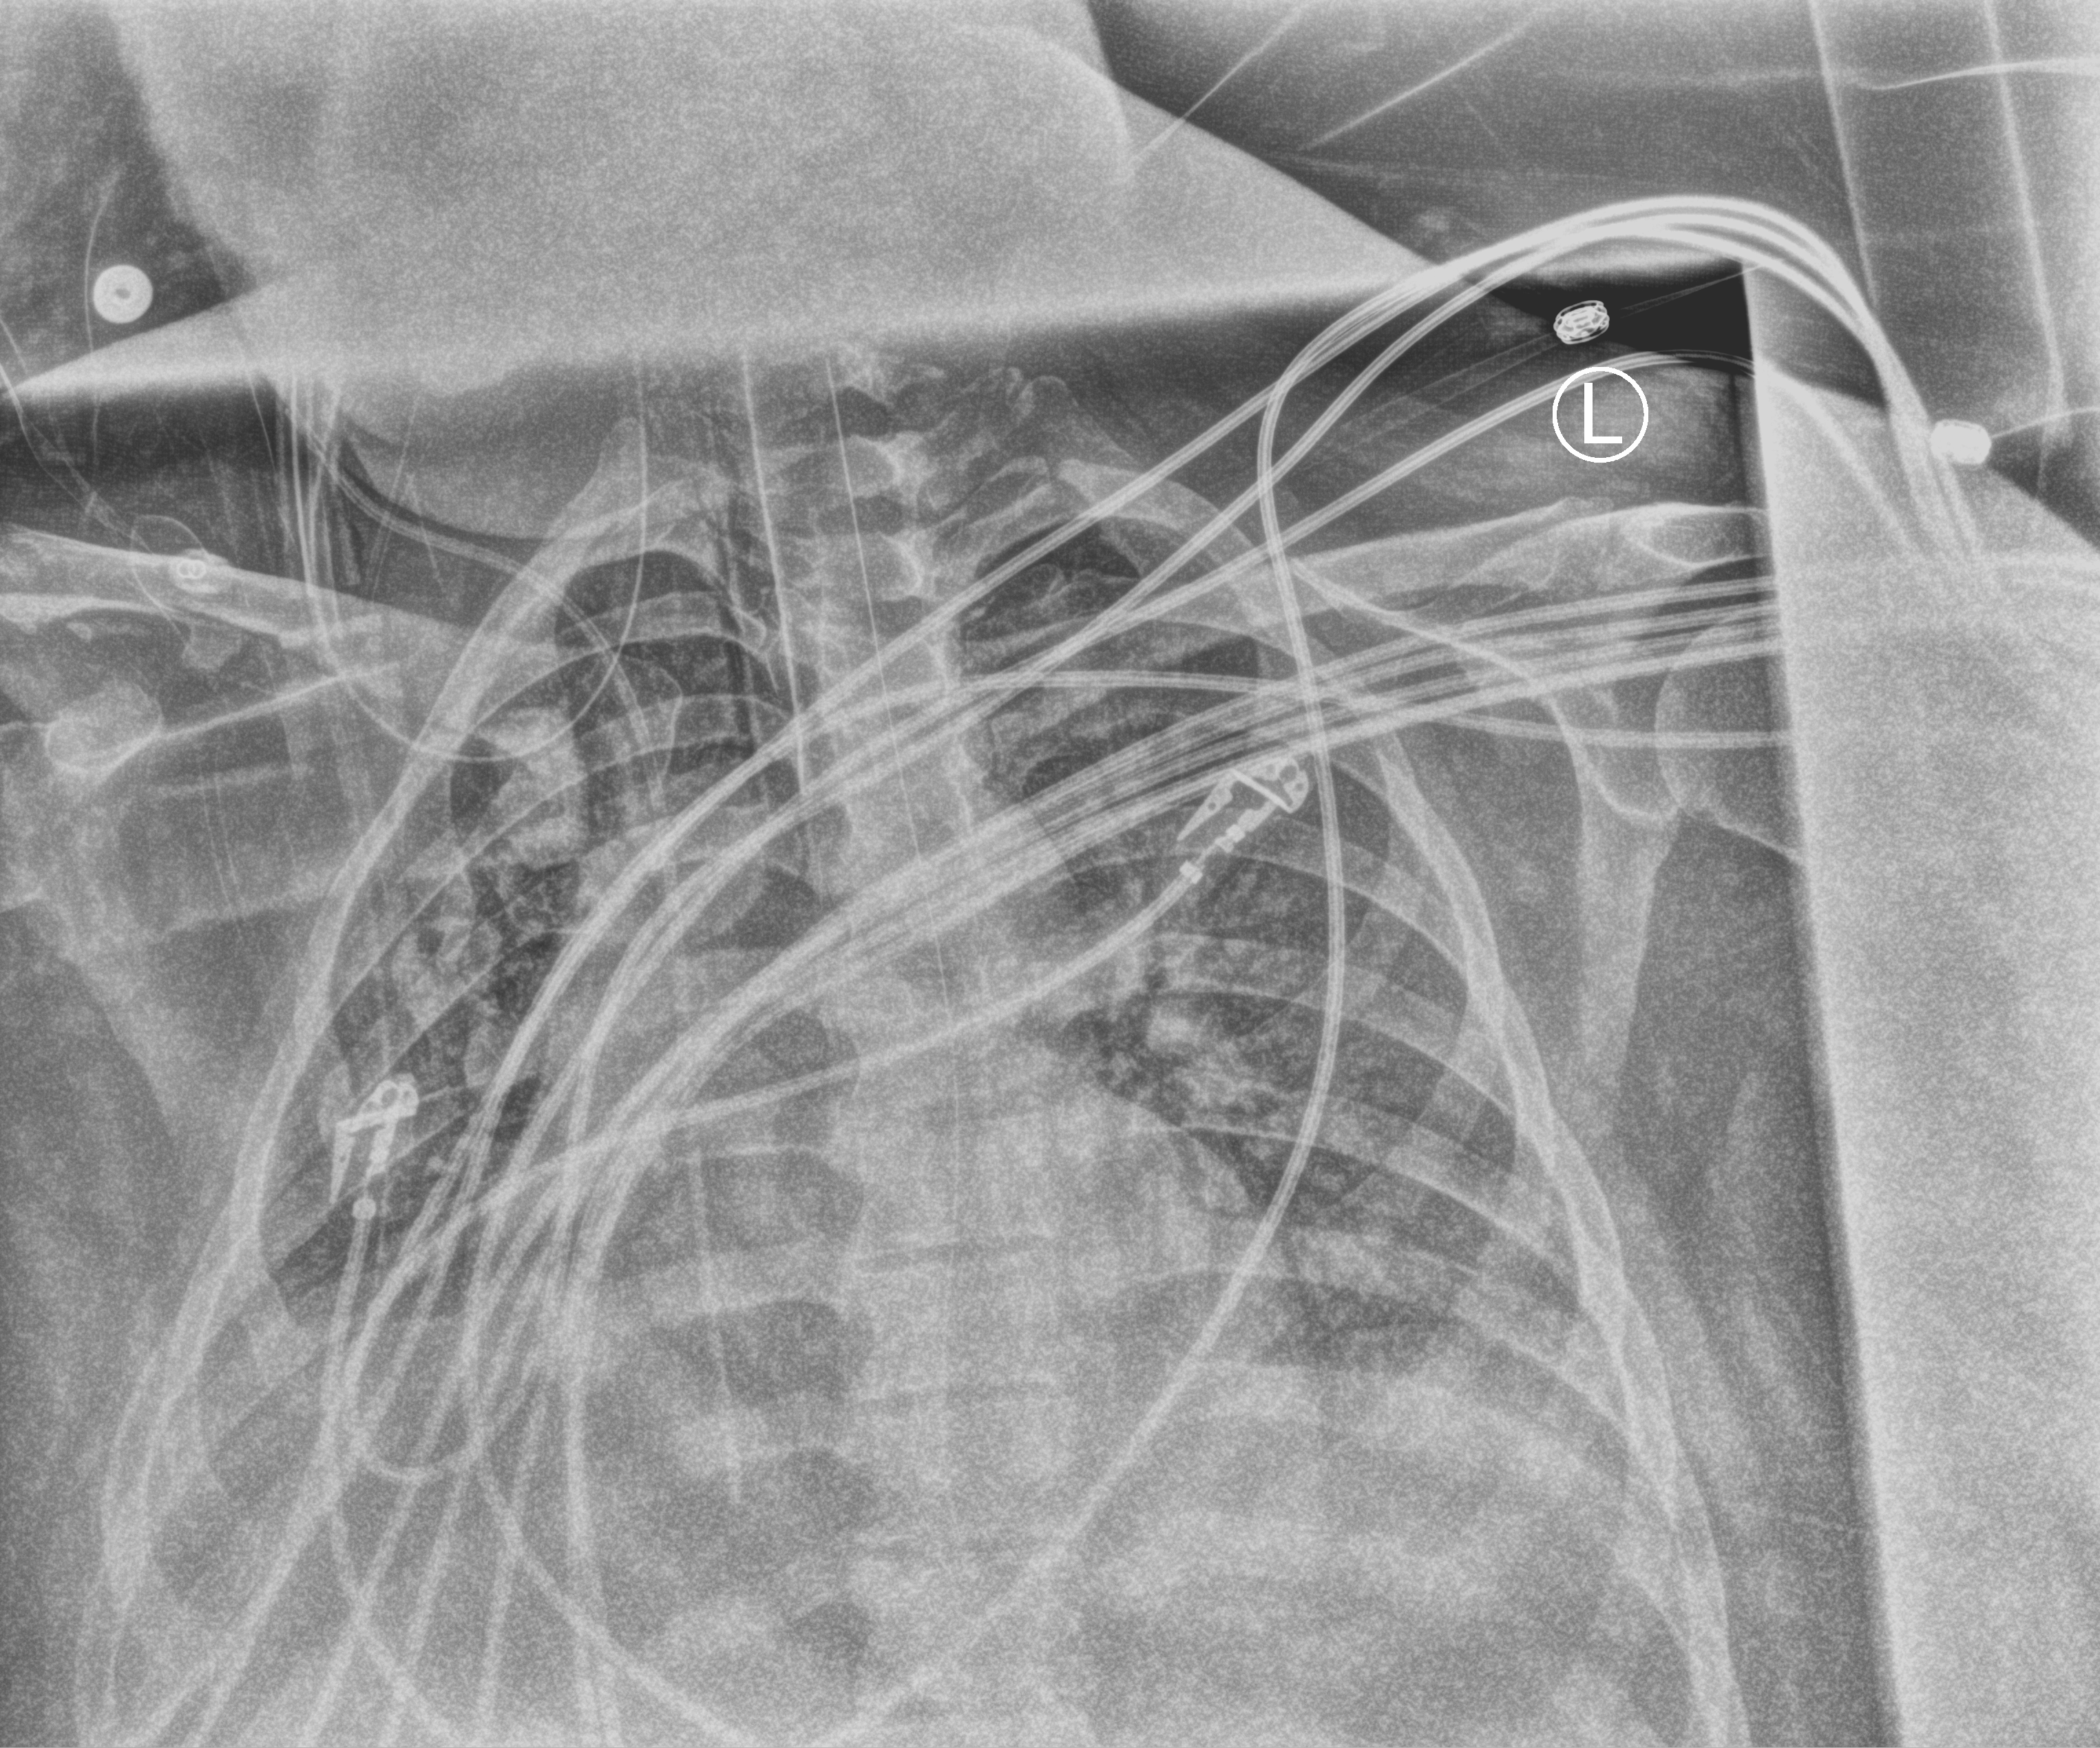
Portable chest radiograph. Female patient hospitalised with COVID-19, age 18–59 years.
Hospital-stay facts (about this admission, not read from this image; timing relative to this image not recorded): mechanically ventilated during this hospital stay: yes; hypertension (admission record): no.